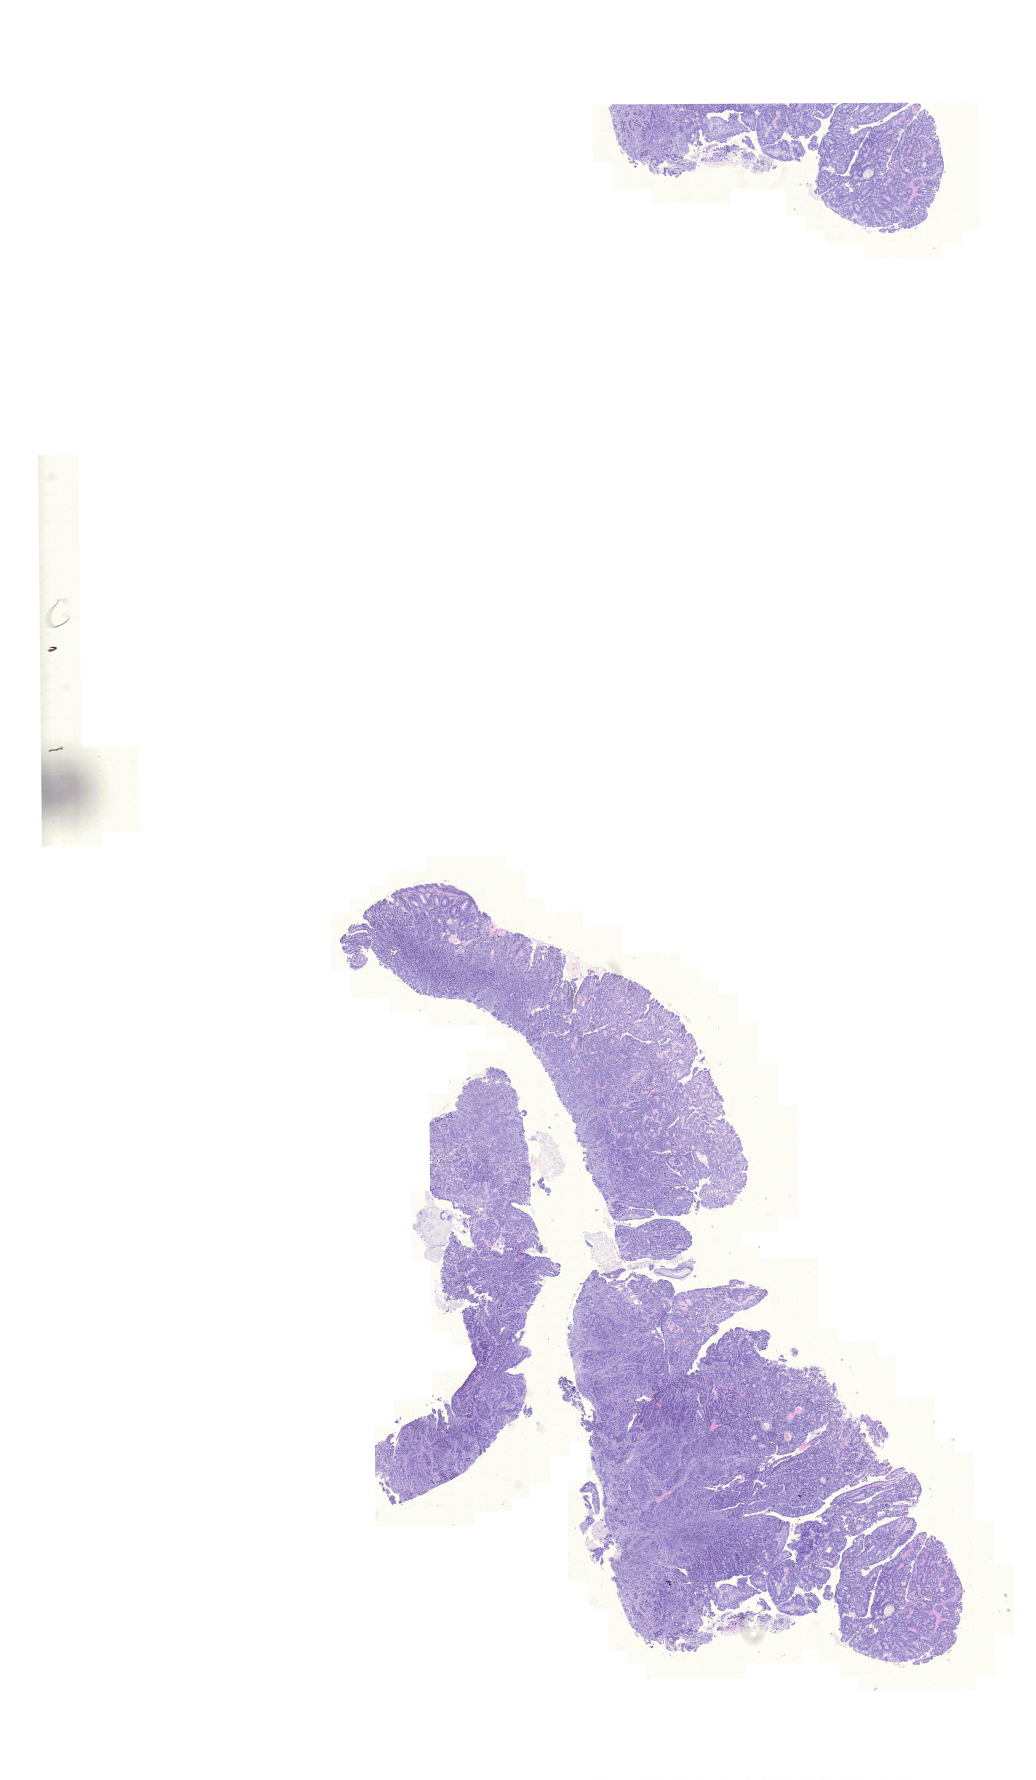
H&E-stained whole-slide image — whole scanned area (about 15.4 x 26.5 mm, slide scanned at 20x) shown as a low-resolution overview, FFPE section, primary tumour sample from the colon. Female patient; age at initial diagnosis 47 years.
Pathologic diagnosis: Mucinous adenocarcinoma (rectosigmoid junction). AJCC pathologic stage: IIIC (6th edition).